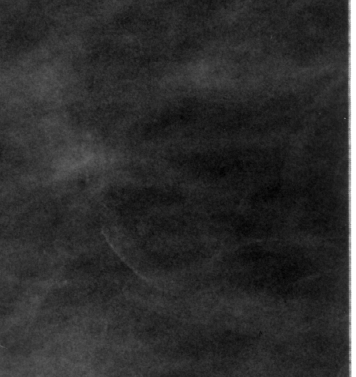
Region of interest cut from a scanned film mammogram (one marked finding); right breast; CC view.
- Finding: calcifications, morphology vascular; BI-RADS assessment category 2; benign; no additional work-up was recommended (benign without callback).